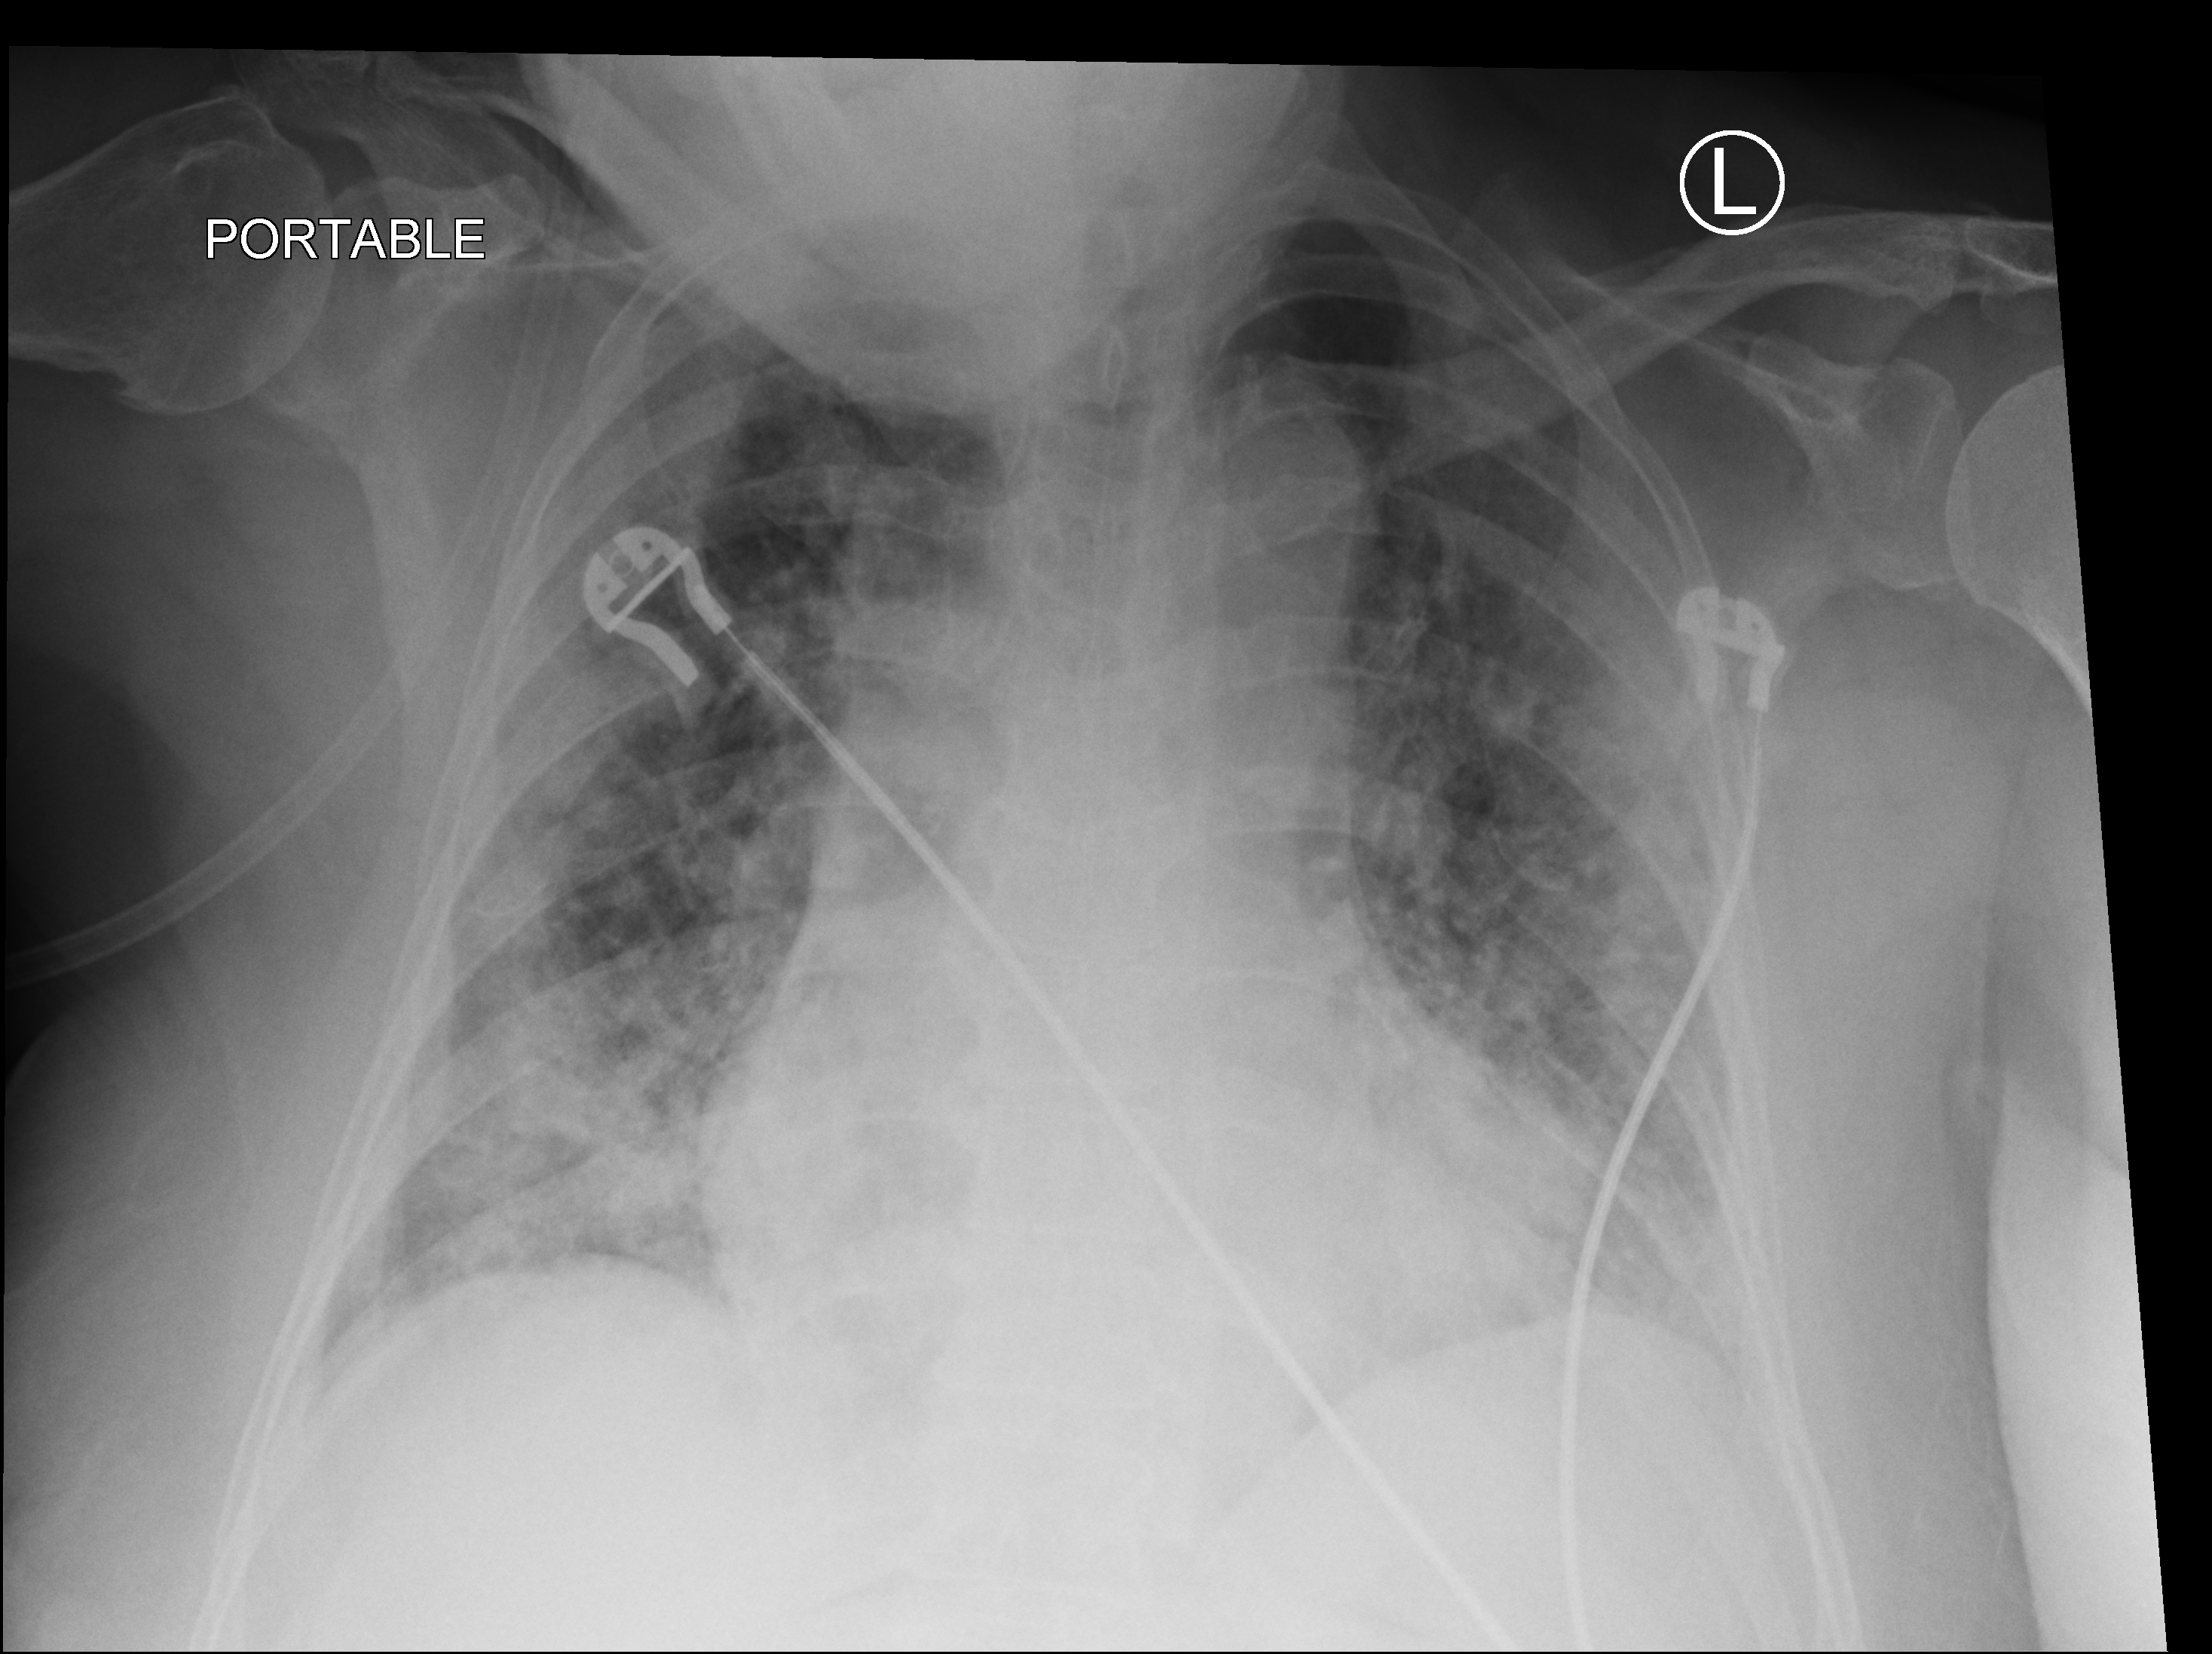
Chest X-ray (portable); anteroposterior (AP) projection. Female patient hospitalised with COVID-19, age 60–74 years.
Hospital-stay facts (about this admission, not read from this image; timing relative to this image not recorded): diabetes (admission record): yes; smoking status (admission record): never; mechanically ventilated during this hospital stay: no.